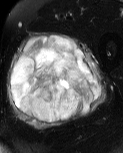
MRI of an extremity soft-tissue mass, one axial slice; slice 28 of 60 in the series (ordered by position); T2-weighted fat-saturated; MR volume resampled by the dataset authors to the PET/CT grid (not the native acquisition matrix); 123 × 153 image matrix, field of view 120 × 149 mm. Male patient. From the clinical record (not read from this slice): histological type: pleiomorphic liposarcoma; grade: high; site of the primary tumour: left thigh.
Annotated regions visible in this slice (expert contour drawn on MRI and transferred to this co-registered scan by the dataset authors):
- gross tumour volume including surrounding oedema: bounding box <6,31,107,130> (left, top, right, bottom; pixels)
- gross tumour volume (mass): <11,36,101,124>